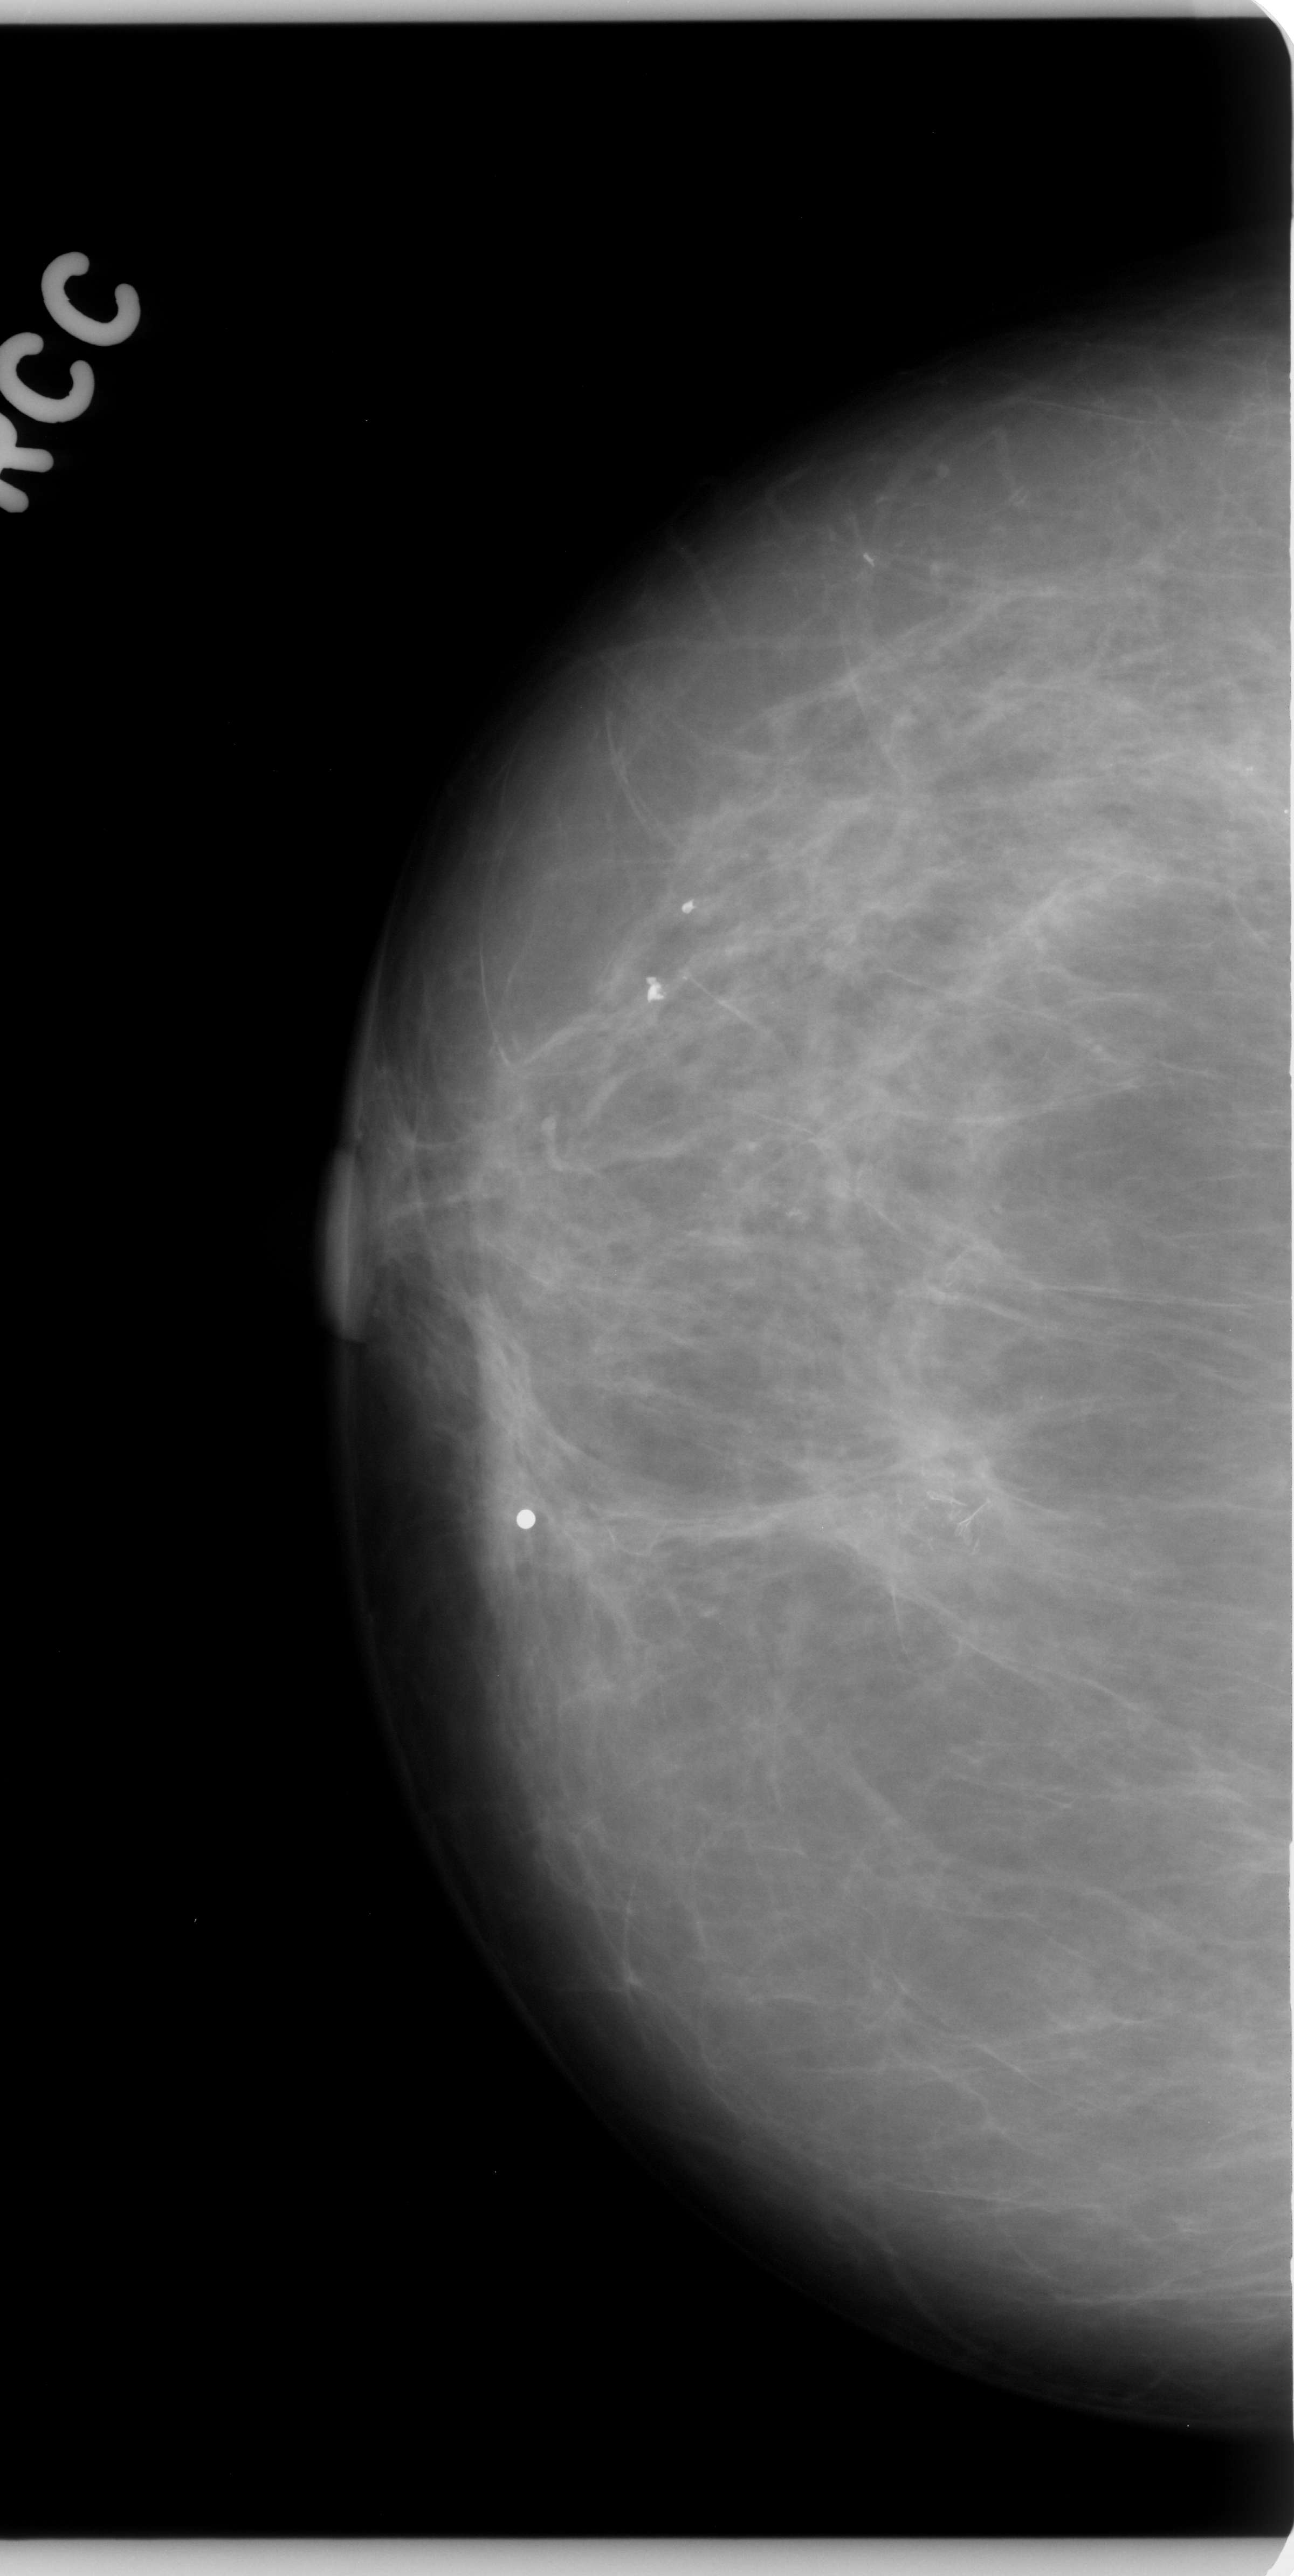
Digitized screen-film mammogram, right breast, CC view.
- Calcifications, morphology fine linear branching, distribution clustered; BI-RADS assessment category 4; subtlety rating 4 on a 1 (subtle) to 5 (obvious) scale; pathology (as recorded): benign.